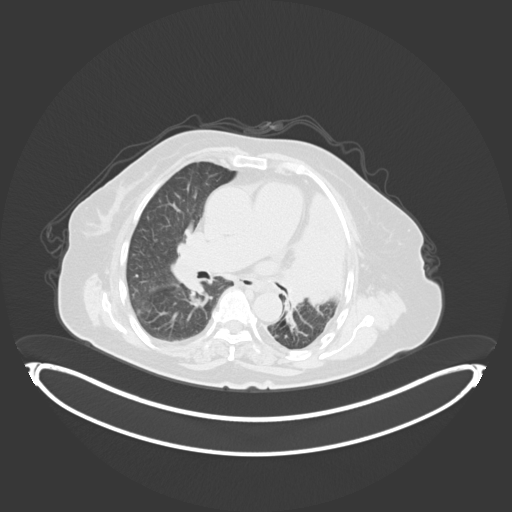
Chest CT, one axial slice; position 200 of 284 along the scan axis; lung window (W 1500 / L -600 HU); 3 mm slice thickness; 512 × 512 image matrix. Female patient, age 75 years. Case-level facts recorded for this patient, not image findings: clinical TNM (as recorded): T3 N3 M1.
Outlined on this slice (rectangle marked by the reading radiologist):
- lung tumour (recorded histology: adenocarcinoma): bounding box (x1, y1, x2, y2) in pixels: (285, 189, 354, 309)